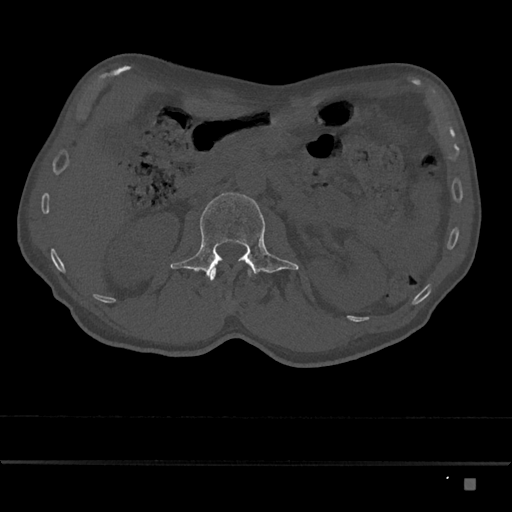
CT including the spine, one axial slice; position 490 of 797 along the scan axis; bone window (W 1800 / L 400 HU); 0.5 mm slice thickness; 512 × 512 image matrix, field of view 390 × 390 mm. Male patient, age 72 years. Case-level facts recorded for this patient, not image findings: primary cancer: prostate.
Structures marked on this image (semi-automatic segmentation, software-assisted and operator-edited):
- L1 vertebra: bounding box (x1, y1, x2, y2) in pixels: (210, 267, 251, 281)
- L2 vertebra: (170, 192, 299, 278)